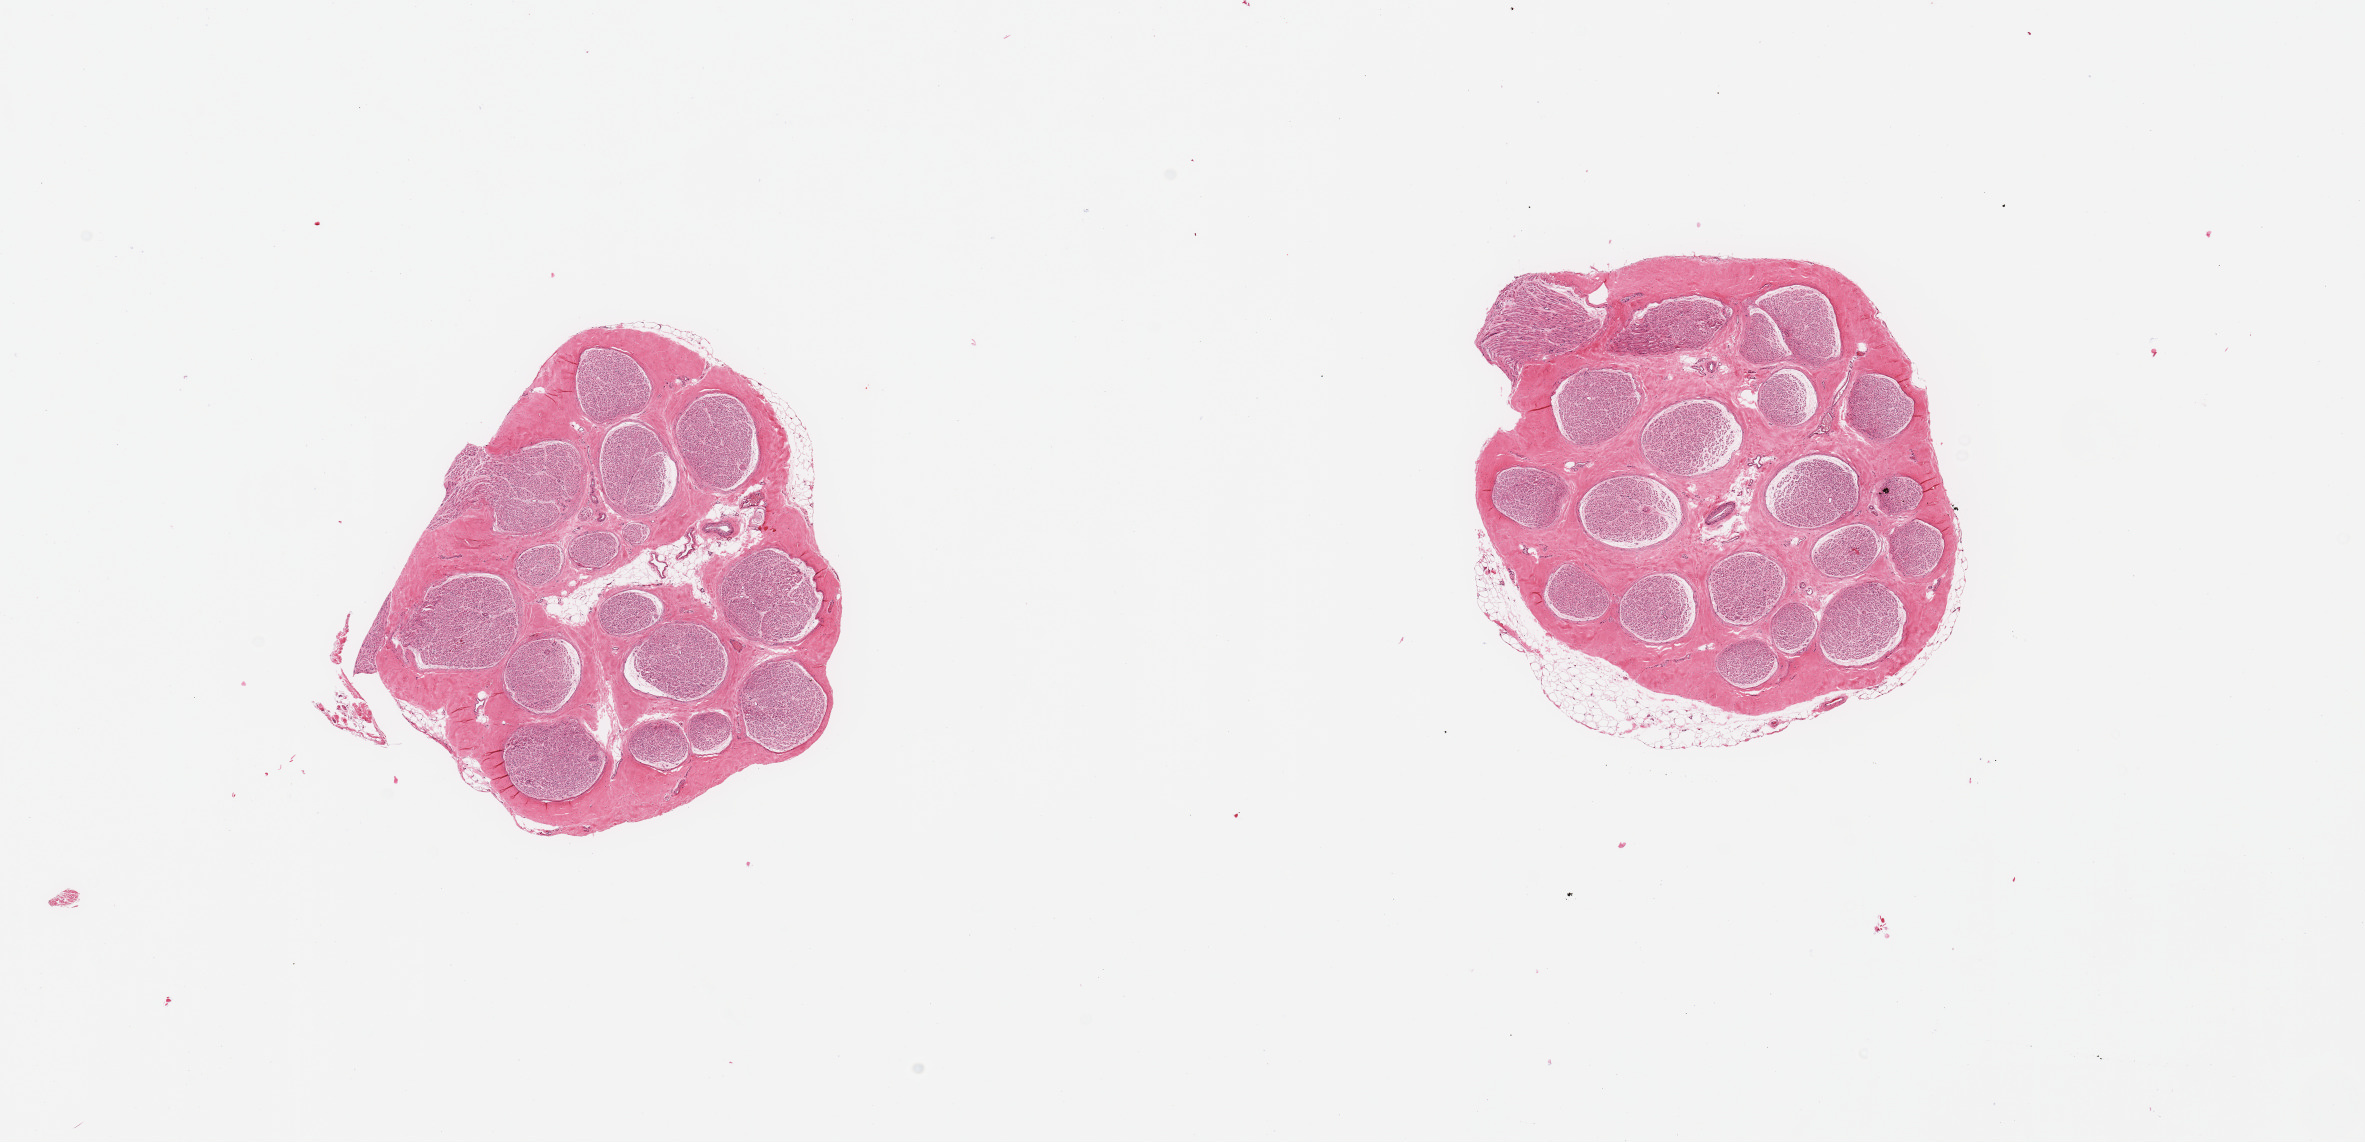
Whole-slide image, haematoxylin and eosin stain, low-resolution overview of the scanned area, about 18.7 x 9.0 mm, PAXgene-fixed, paraffin-embedded tissue, sampled site (target tissue): tibial nerve, tissue donor sample. Male donor.
Review note (as recorded): 2 pieces; 30% internal fibrous stroma; 10% internal fat on 1, 10% external fat on other.